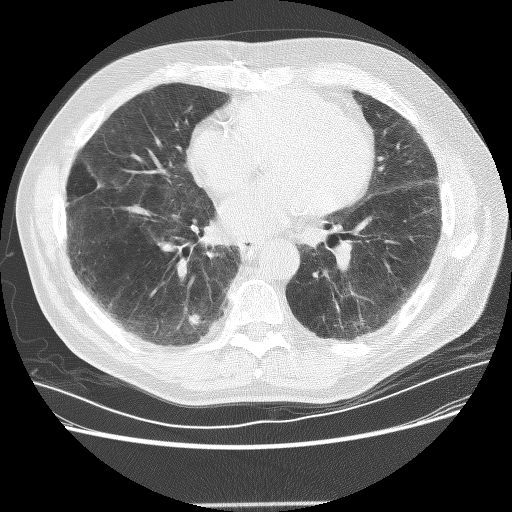
Chest CT (low-dose screening protocol), one axial image, baseline annual screen, lung window (W 1500 / L -600 HU), 2.5 mm slice thickness, 512 × 512 image matrix, field of view 370 × 370 mm. Male, age 72 years at enrolment. Former smoker at enrolment.
Expert reader's lesion annotation, box from (x=170, y=307) to (x=210, y=343) px. The screening reader recorded 2 non-calcified nodules or masses ≥4 mm on this exam (right lower lobe, left lower lobe); which of them this box marks is not recorded. Official screen result: positive, change unspecified: nodule(s) >= 4 mm or enlarging nodule(s), mass(es), or other non-specific abnormalities suspicious for lung cancer. Later outcome: lung cancer diagnosed 436 days after this screen (after the second annual screen) — squamous cell carcinoma, NOS, right lower lobe, poorly differentiated (G3), stage IB (AJCC 6th edition), 42 mm at pathology.